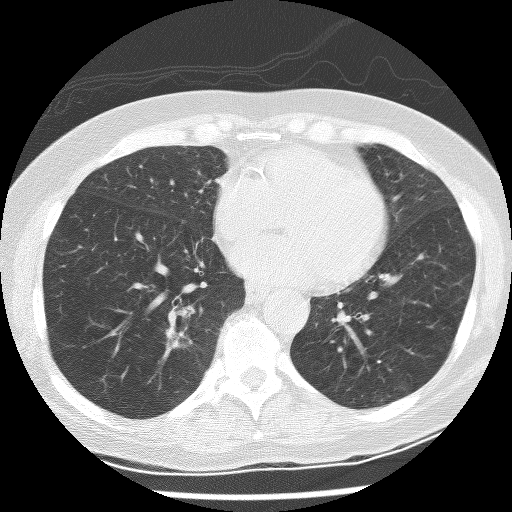
Chest CT (low-dose screening protocol), one axial image. Baseline screening round. Lung window (W 1500 / L -600 HU). 2.5 mm slice thickness. Female, age 60 years at enrolment.
Expert-annotated lung lesion, bounding box [x1, y1, x2, y2] px = [157, 322, 203, 358]. Screening reader's record for this exam (one nodule recorded; not confirmed to be the boxed lesion): non-calcified nodule or mass ≥4 mm, right lower lobe, 10 × 6 mm, spiculated (stellate) margins, mixed attenuation. Participant outcome: lung cancer diagnosed 275 days after this screen — adenocarcinoma with squamous metaplasia, right lower lobe, poorly differentiated (G3), stage IA (AJCC 6th edition), 23 mm at pathology.